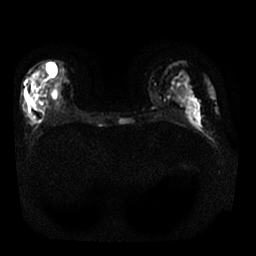
Breast MRI, one axial slice. Position 12 of 30 along the scan axis. Diffusion-weighted series; image 2 of 4 stored at this slice position (different b-values; order by instance number). 1.5 T. 4 mm slice thickness. 256 × 256 image matrix. Female patient.
Annotated regions visible in this slice (outlined manually by an expert reader):
- tumour on diffusion-weighted imaging: box from (x=31, y=88) to (x=46, y=114) px